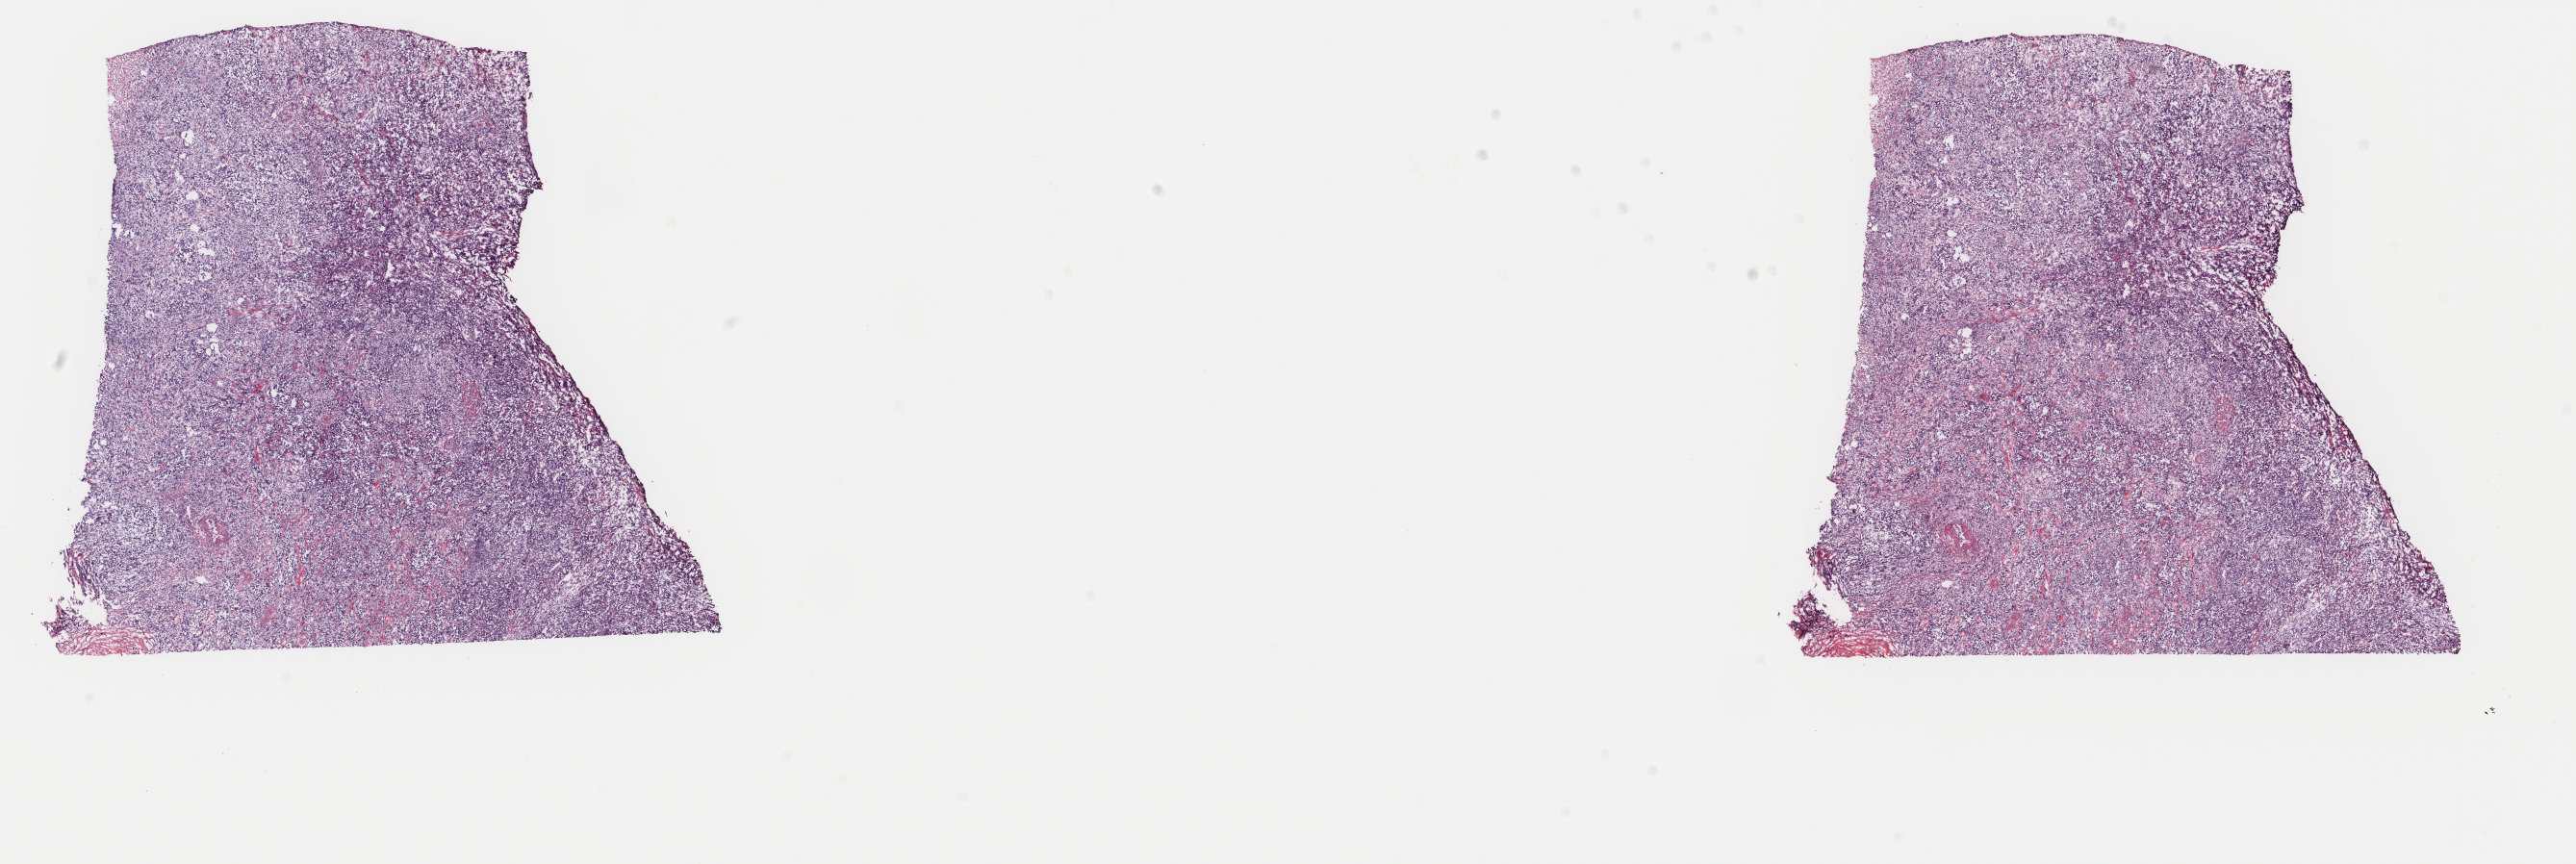
Whole-slide histology image, H&E-stained, shown as a low-resolution overview of the whole scanned area (about 21.2 x 7.1 mm, from a 40x scan). Frozen section from the top of the tissue portion. Sample: primary tumour, bladder. Male patient; age at initial diagnosis 87 years. Histologic grade: high grade. Slide review estimates, as recorded: tumour cells 70%, tumour nuclei 70%, normal cells 0%, stromal cells 30%, necrosis 0%. Infiltration values recorded for this section: lymphocyte infiltration 0%, monocyte infiltration 0%, neutrophil infiltration 0%.
- AJCC pathologic stage: IV
- lymph nodes positive (case pathology): 4 of 10 examined
- histologic diagnosis: Transitional cell carcinoma